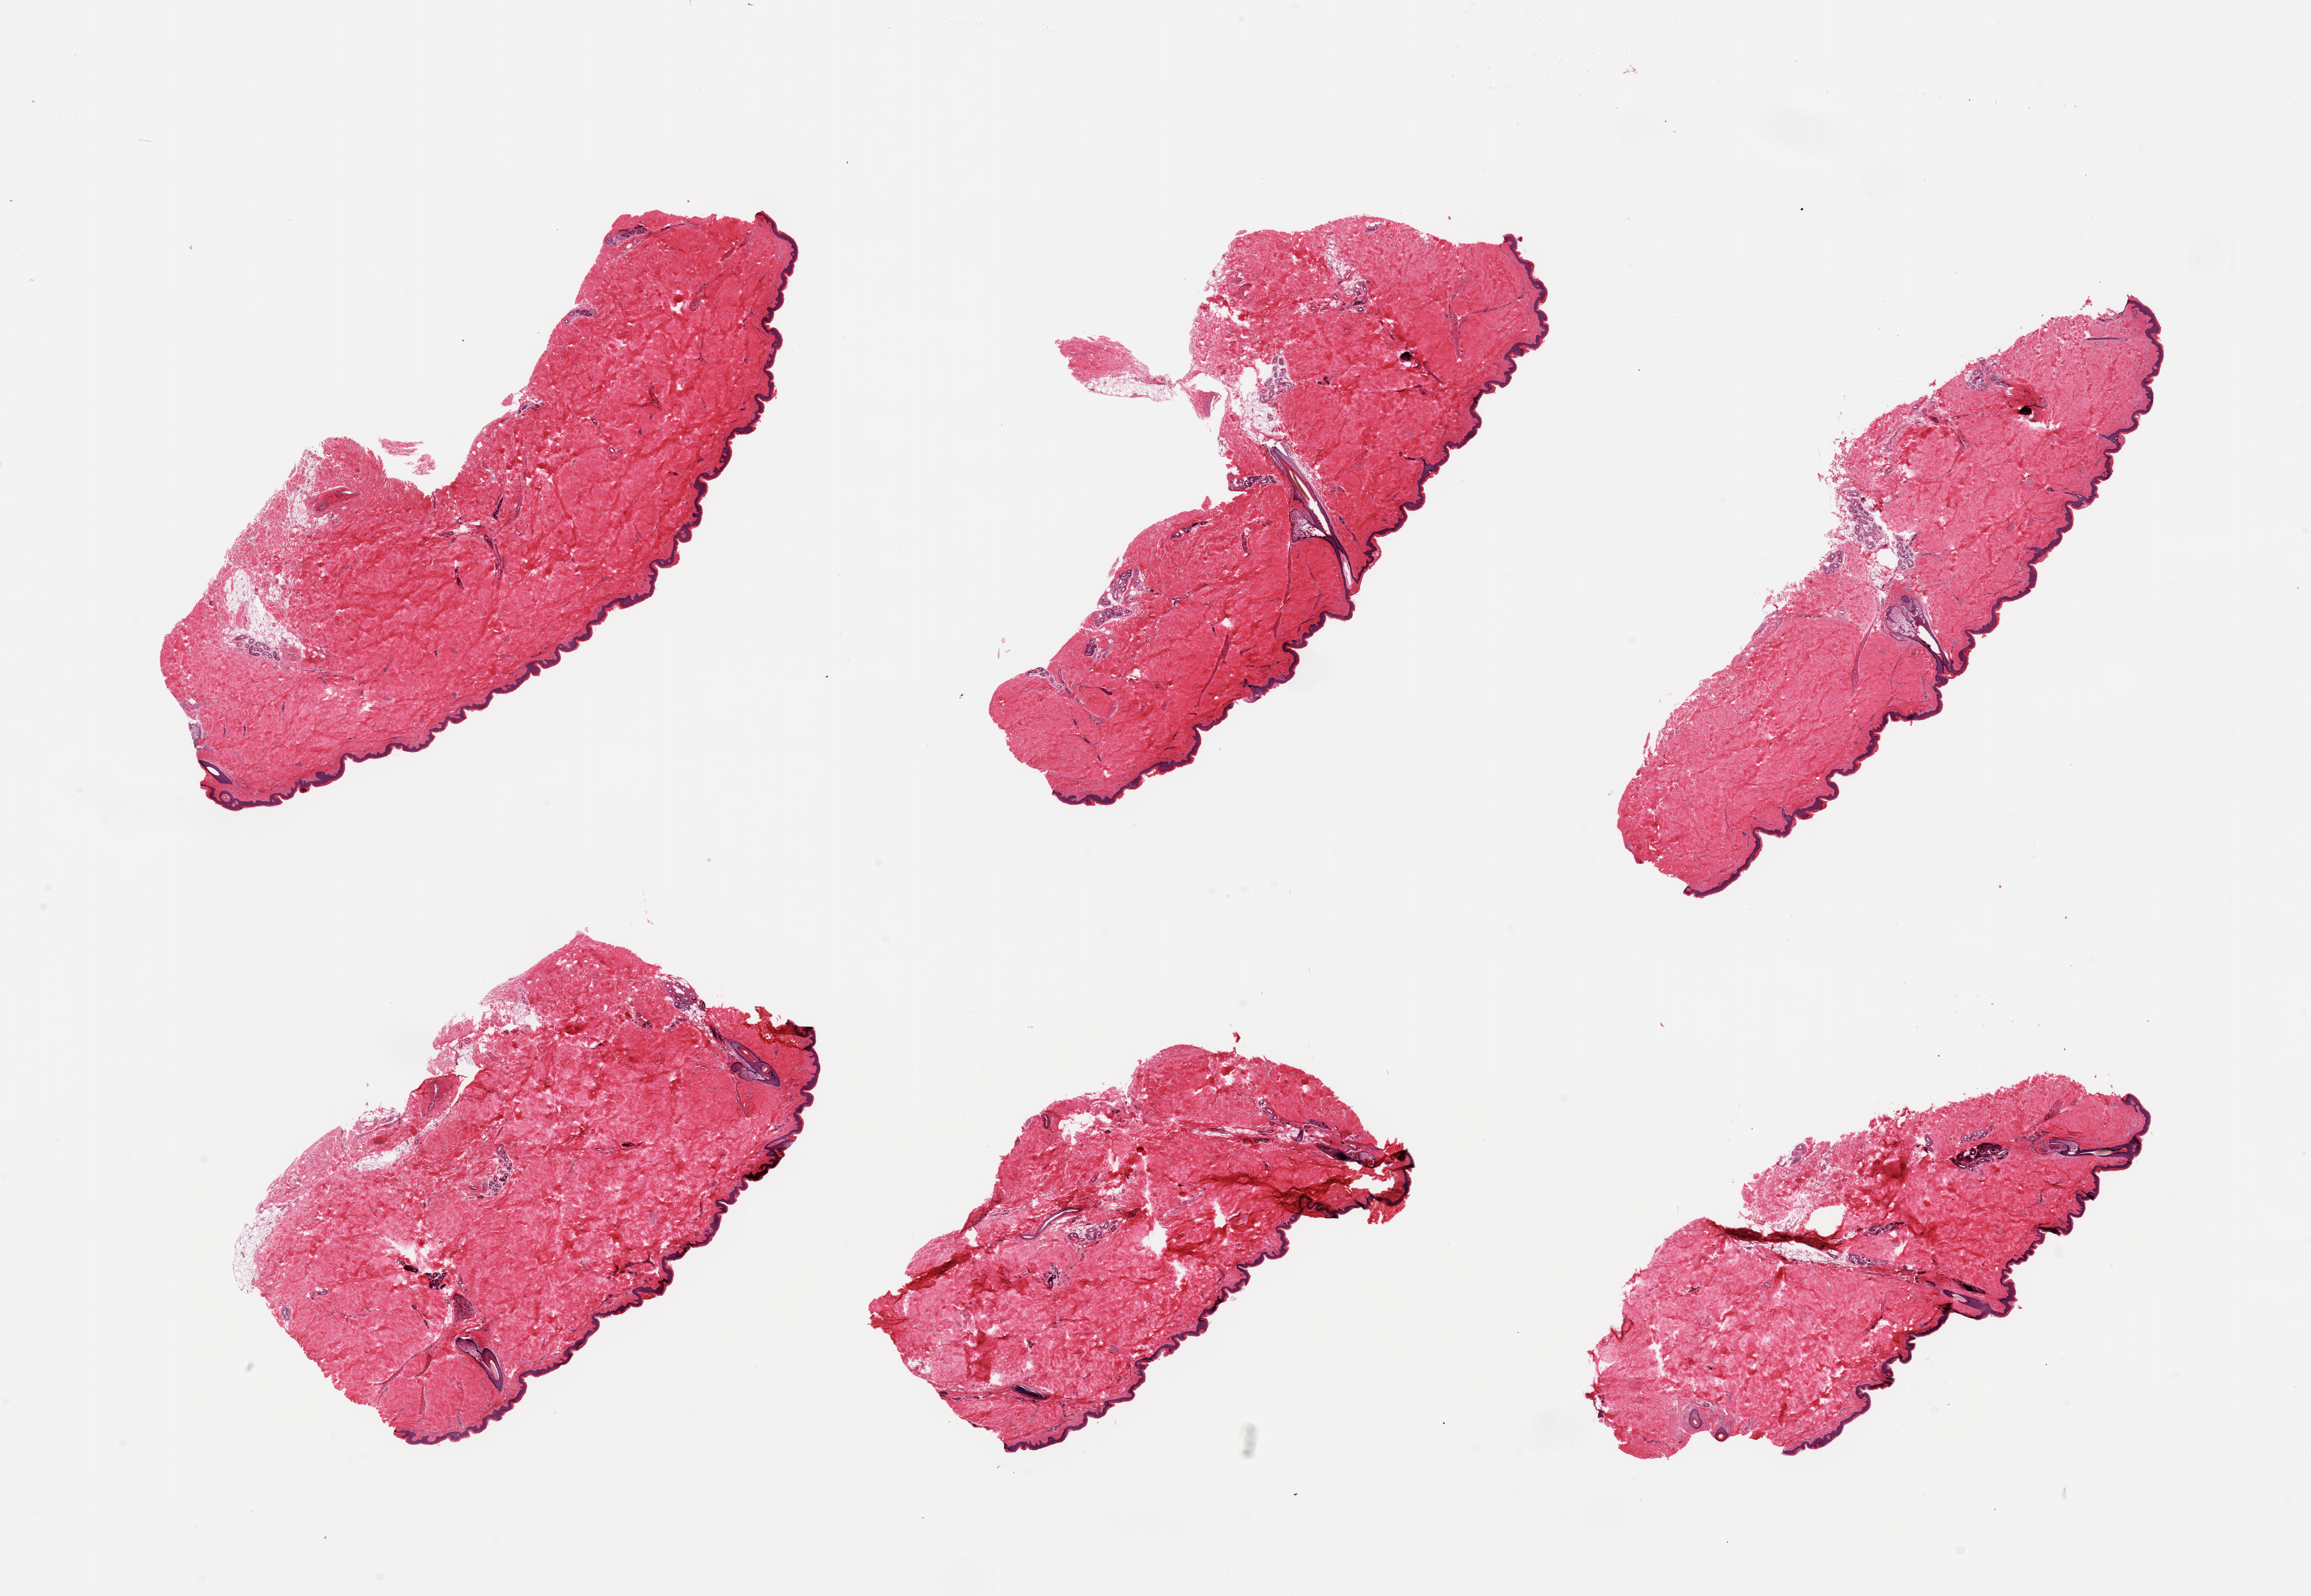
Digitized haematoxylin and eosin-stained section, whole scanned area (about 27.6 x 19.0 mm) shown as a low-resolution overview. PAXgene-fixed paraffin-embedded (PFPE) section. Target tissue: skin of lower leg. Tissue donor sample. Donor: male.
Pathologist's review note for this sample: 6 pieces; well trimmed, epidermis measures about 34 microns.